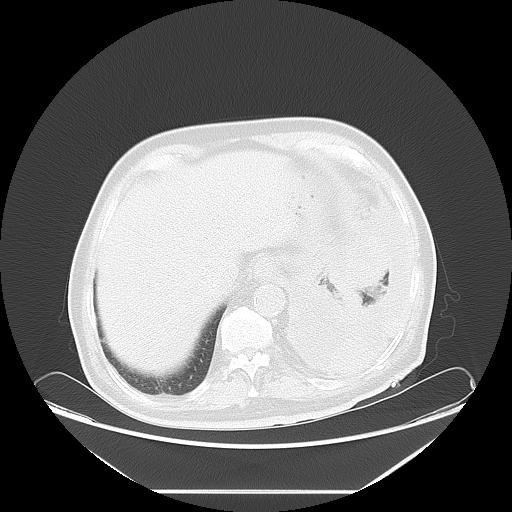
Chest CT, one axial slice; slice 14 of 63 in the series (ordered by position); reconstruction kernel LUNG; lung window (W 1500 / L -600 HU); 5 mm slice thickness; 512 × 512 image matrix, field of view 448 × 448 mm. Male patient, age 67 years. Case-level facts recorded for this patient, not image findings: clinical TNM (as recorded): T1b N1 M1a; histopathological grade: G3.
Annotated regions visible in this slice (rectangle marked by the reading radiologist):
- lung tumour (recorded histology: small cell carcinoma): bounding box (x1, y1, x2, y2) in pixels: (320, 232, 392, 299)